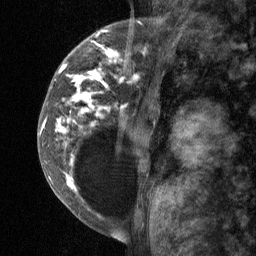
Breast MRI (dynamic contrast-enhanced), one sagittal slice; position 19 of 64 along the scan axis; dynamic contrast-enhanced study with each time point stored as its own series, time point 2 of 3 at this slice position (early post-contrast, ordered by acquisition time); 1.5 T; TE 4.8 ms, TR 27 ms; 256 × 256 image matrix, field of view 180 × 180 mm. Female patient, age 34 years. From the clinical record (not read from this slice): setting: breast cancer imaged before/during neoadjuvant chemotherapy; receptor status: HR-positive, HER2-negative.
Annotated regions visible in this slice (semi-automatically segmented with operator editing):
- analysis volume of interest (the breast-tissue region the enhancement analysis was run in; not a lesion): box from (x=41, y=23) to (x=157, y=197) px
- tumour enhancement mask (voxels above the 90 % enhancement threshold inside the analysis volume of interest): (x=42, y=31)–(x=145, y=192)